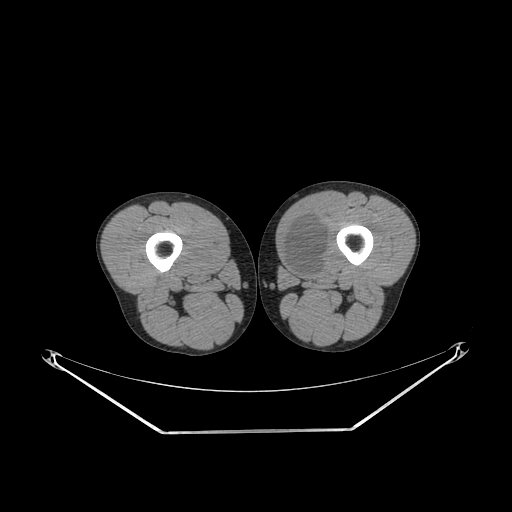
CT of an extremity soft-tissue mass (from a PET/CT study), one axial slice; position 237 of 311 along the scan axis; reconstruction kernel SOFT; soft-tissue window (W 400 / L 40 HU); 512 × 512 image matrix, field of view 500 × 500 mm. Male patient. From the clinical record (not read from this slice): histological type: mixoid liposarcoma; grade: low; site of the primary tumour: left thigh.
Outlined on this slice (expert contour drawn on MRI and transferred to this co-registered scan by the dataset authors):
- gross tumour volume (mass): bounding box (x1, y1, x2, y2) in pixels: (283, 215, 328, 277)